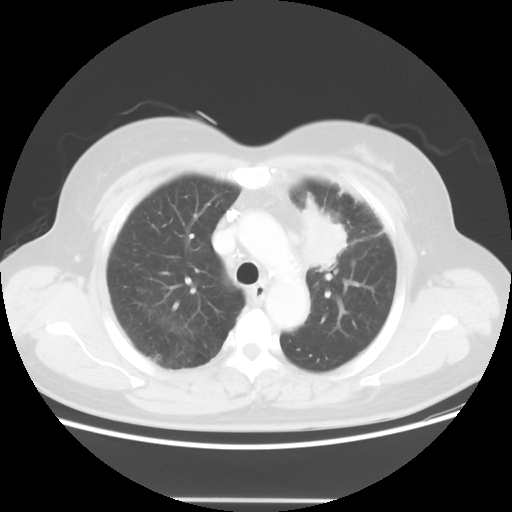
Chest CT, one axial slice; position 40 of 52 along the scan axis; lung window (W 1500 / L -600 HU); 512 × 512 image matrix, field of view 382 × 382 mm. Patient: female, 52 years. Case-level facts recorded for this patient, not image findings: clinical TNM (as recorded): T2 N3 M0.
Annotated regions visible in this slice (bounding box drawn by a radiologist):
- lung tumour (recorded histology: adenocarcinoma): box from (x=294, y=189) to (x=349, y=275) px